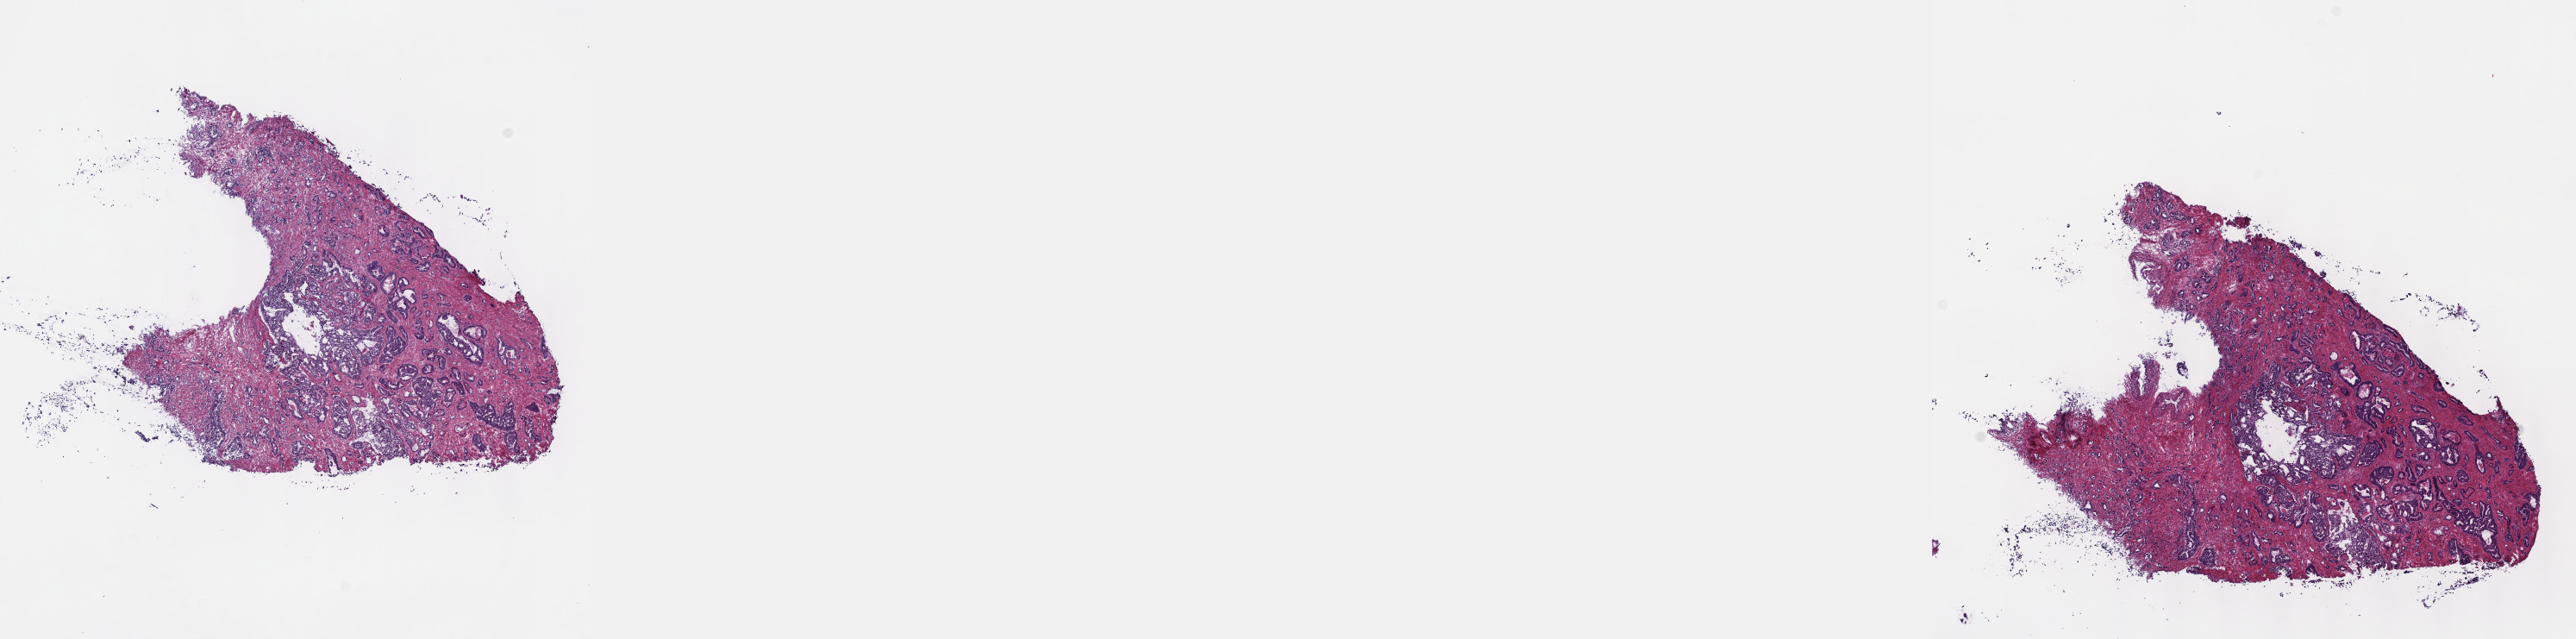
Whole-slide histology image, H&E — a low-resolution overview of the entire scanned area, about 24.1 x 6.0 mm. Frozen section from the top of the tissue portion. Primary tumour sample from the prostate. Male patient; age at initial diagnosis 59 years. Gleason score: 9 (4+5). Pathologist review of this section (percent, as recorded): tumour cells 50%, tumour nuclei 60%, normal cells 0%, stromal cells 50%, necrosis 0%. Infiltration values recorded for this section: lymphocyte infiltration 0%, monocyte infiltration 0%, neutrophil infiltration 0%.
Histologic diagnosis: Adenocarcinoma, NOS (prostate gland).